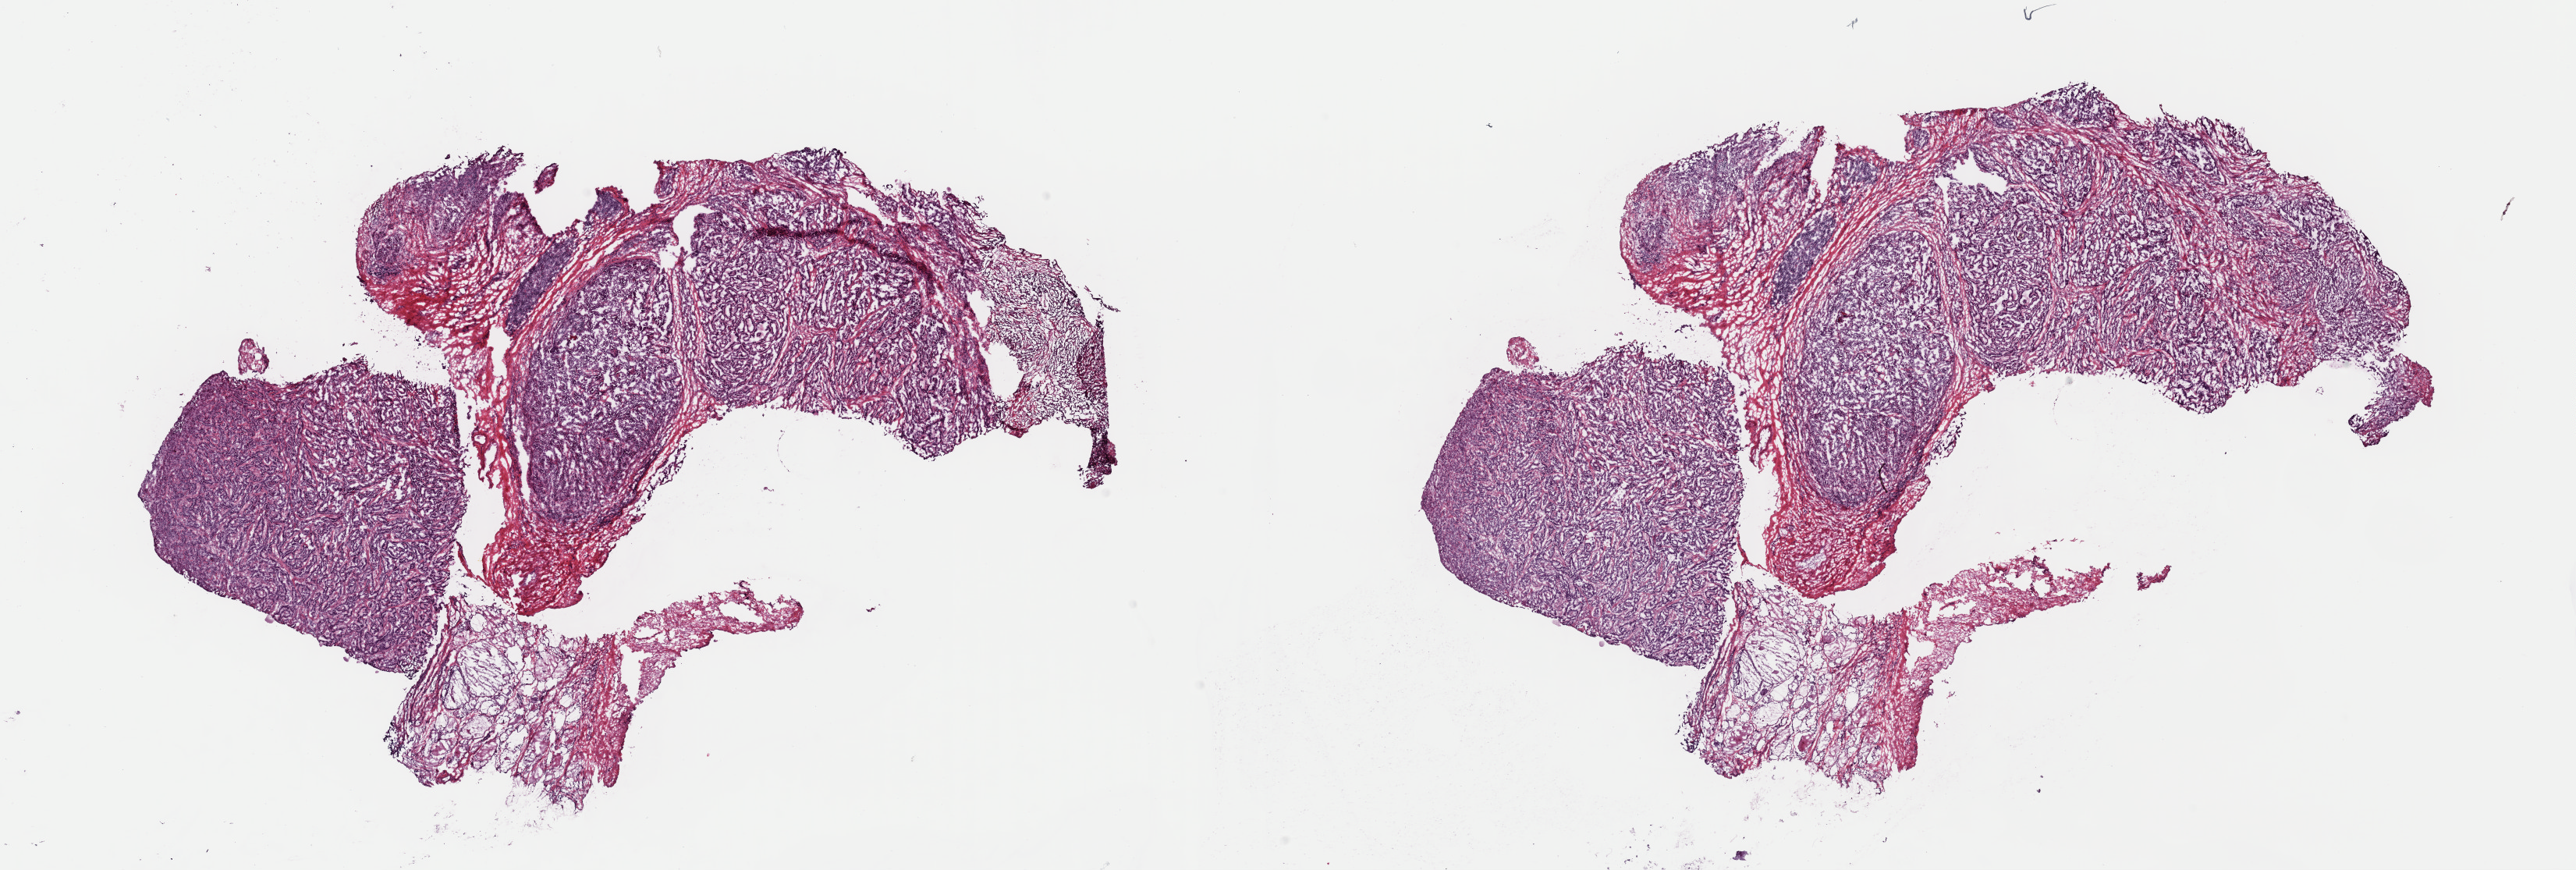
Whole-slide histology image, Hematoxylin and eosin (H&E) stained, low-resolution overview of the scanned area, about 26.1 x 8.8 mm; frozen section; thyroid, primary tumour sample. Female, age 79 years at initial diagnosis. Composition of this section per pathologist review: tumour cells 80%, tumour nuclei 80%.
Diagnosis: Papillary adenocarcinoma, NOS (thyroid gland).